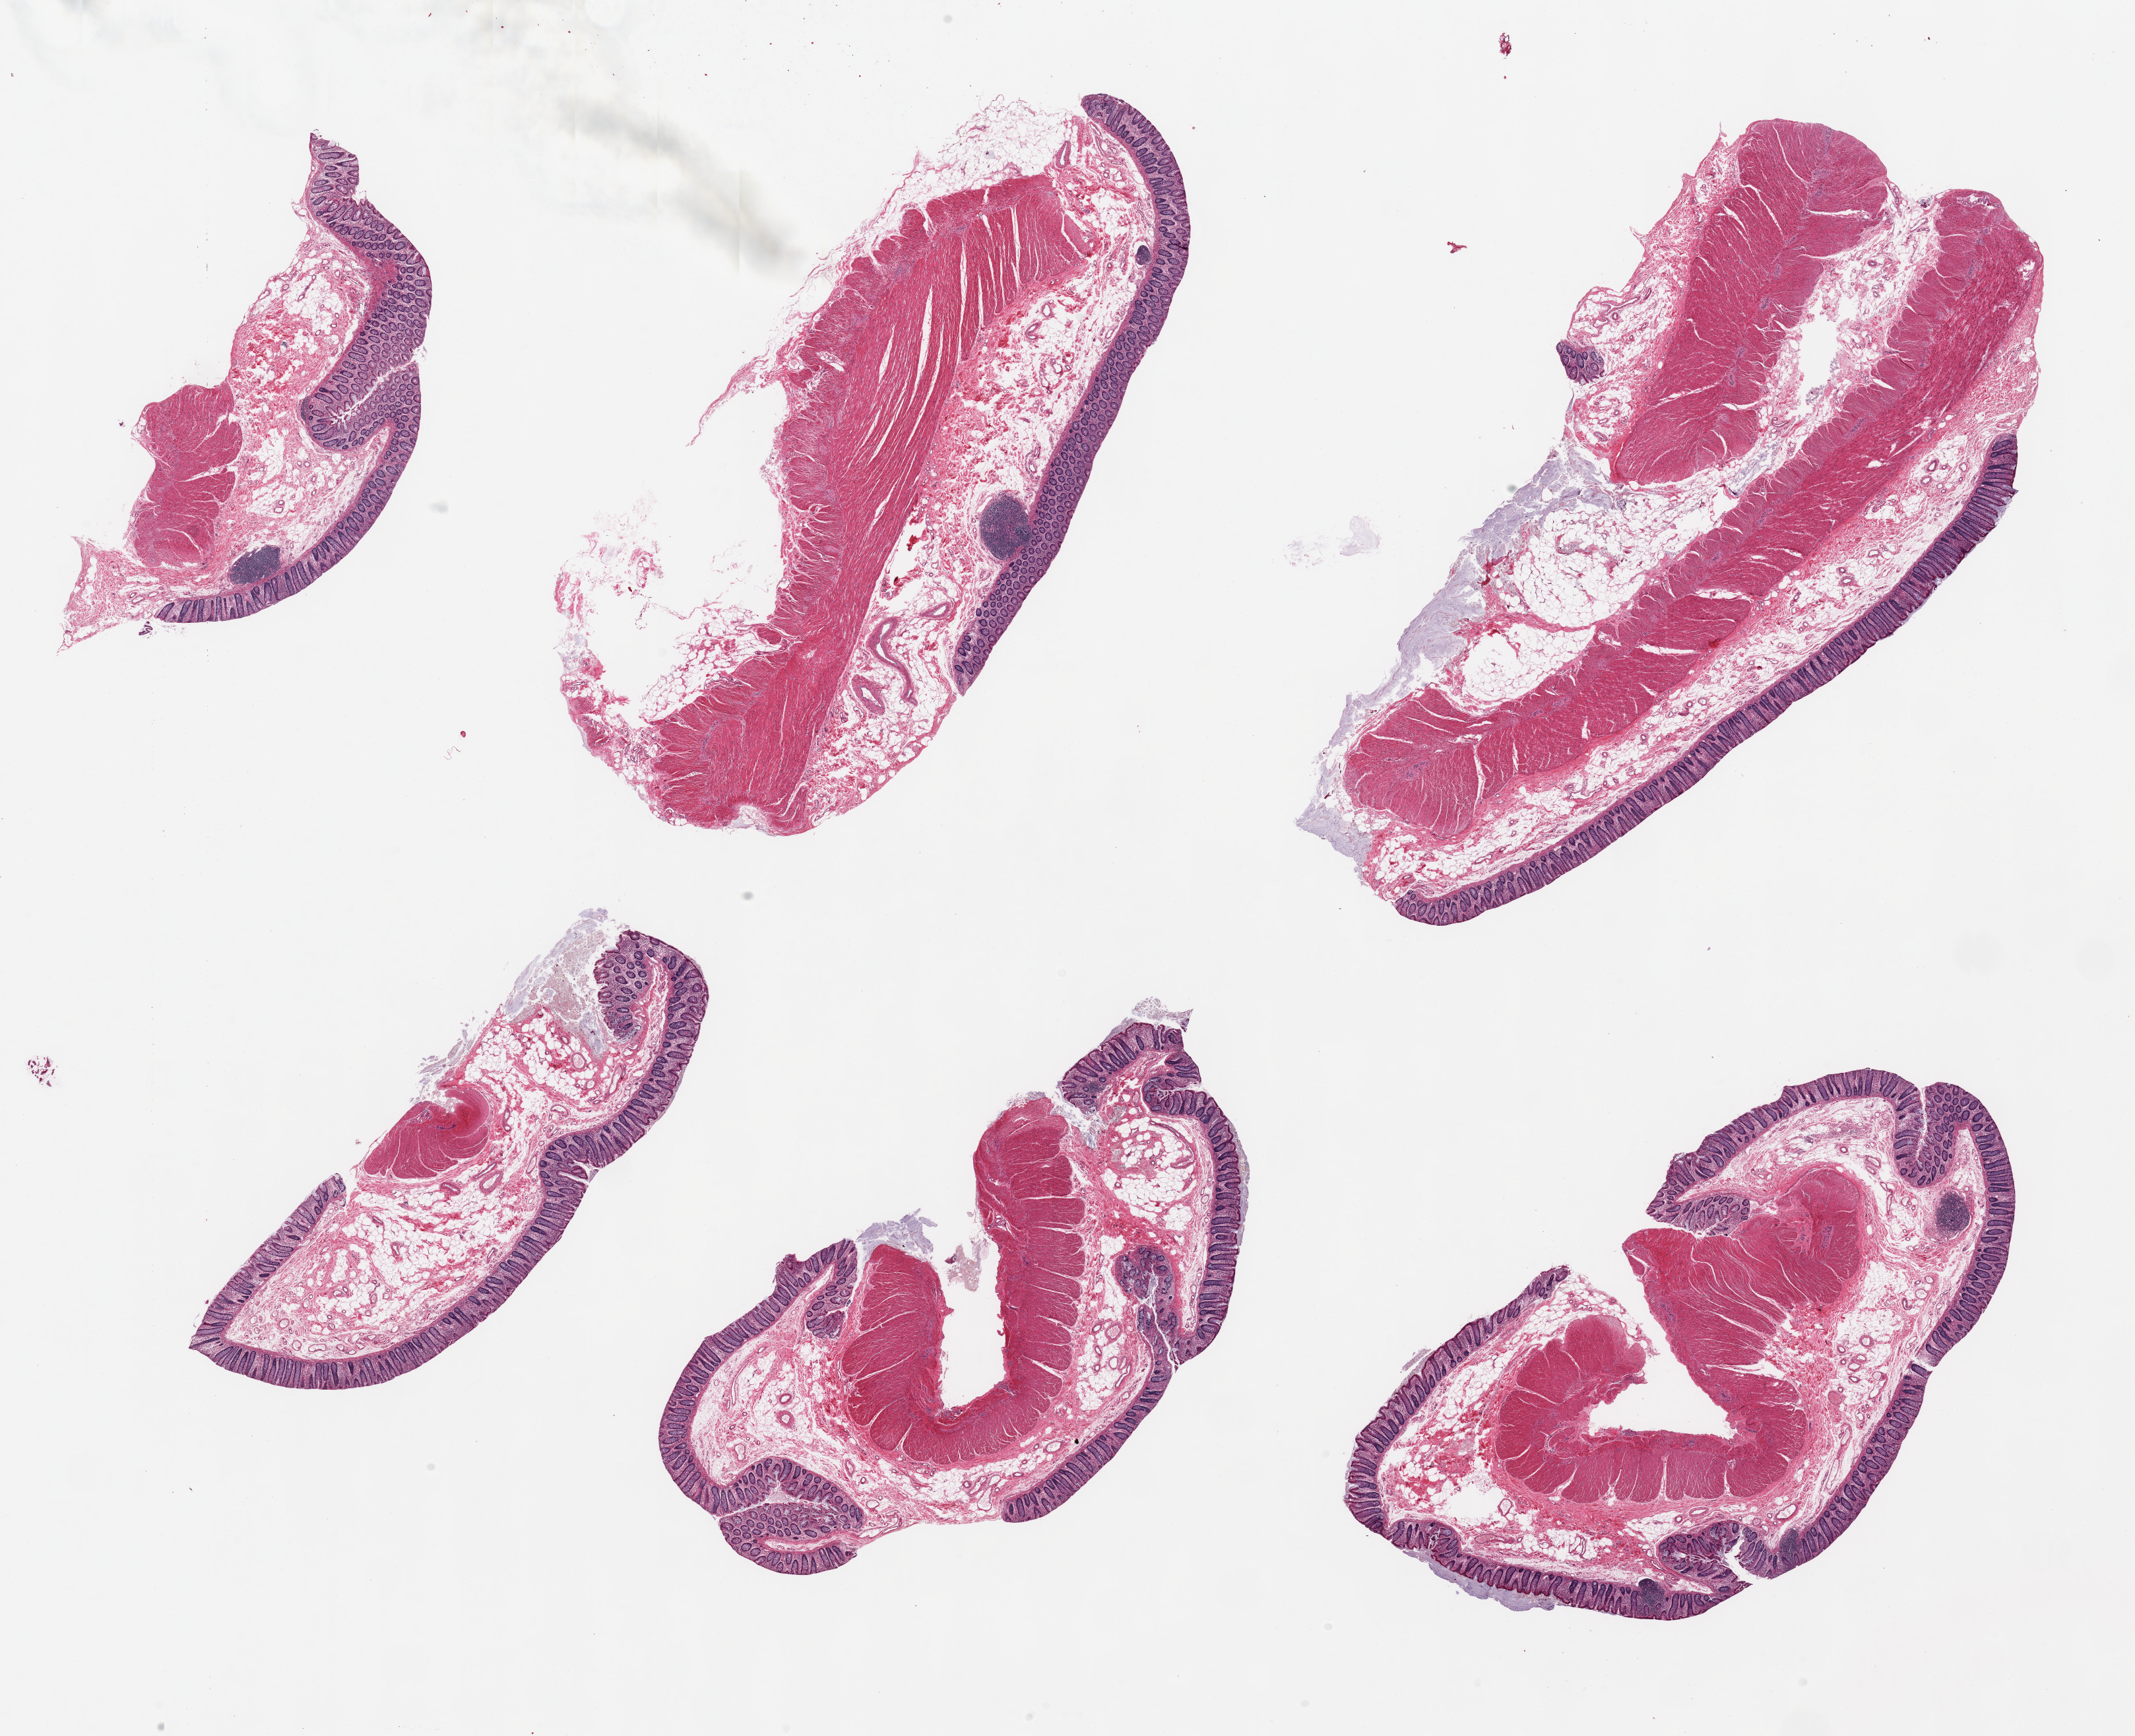
Digitized haematoxylin and eosin-stained section, a low-resolution overview of the entire scanned area, about 25.6 x 20.8 mm, PAXgene-fixed paraffin-embedded (PFPE) section, target tissue: transverse colon, tissue donor sample. Donor sex: male.
Review note (as recorded): 6 pieces; variable representation of mucosa/submucosa/muscularis, small amount of adherent mucus.